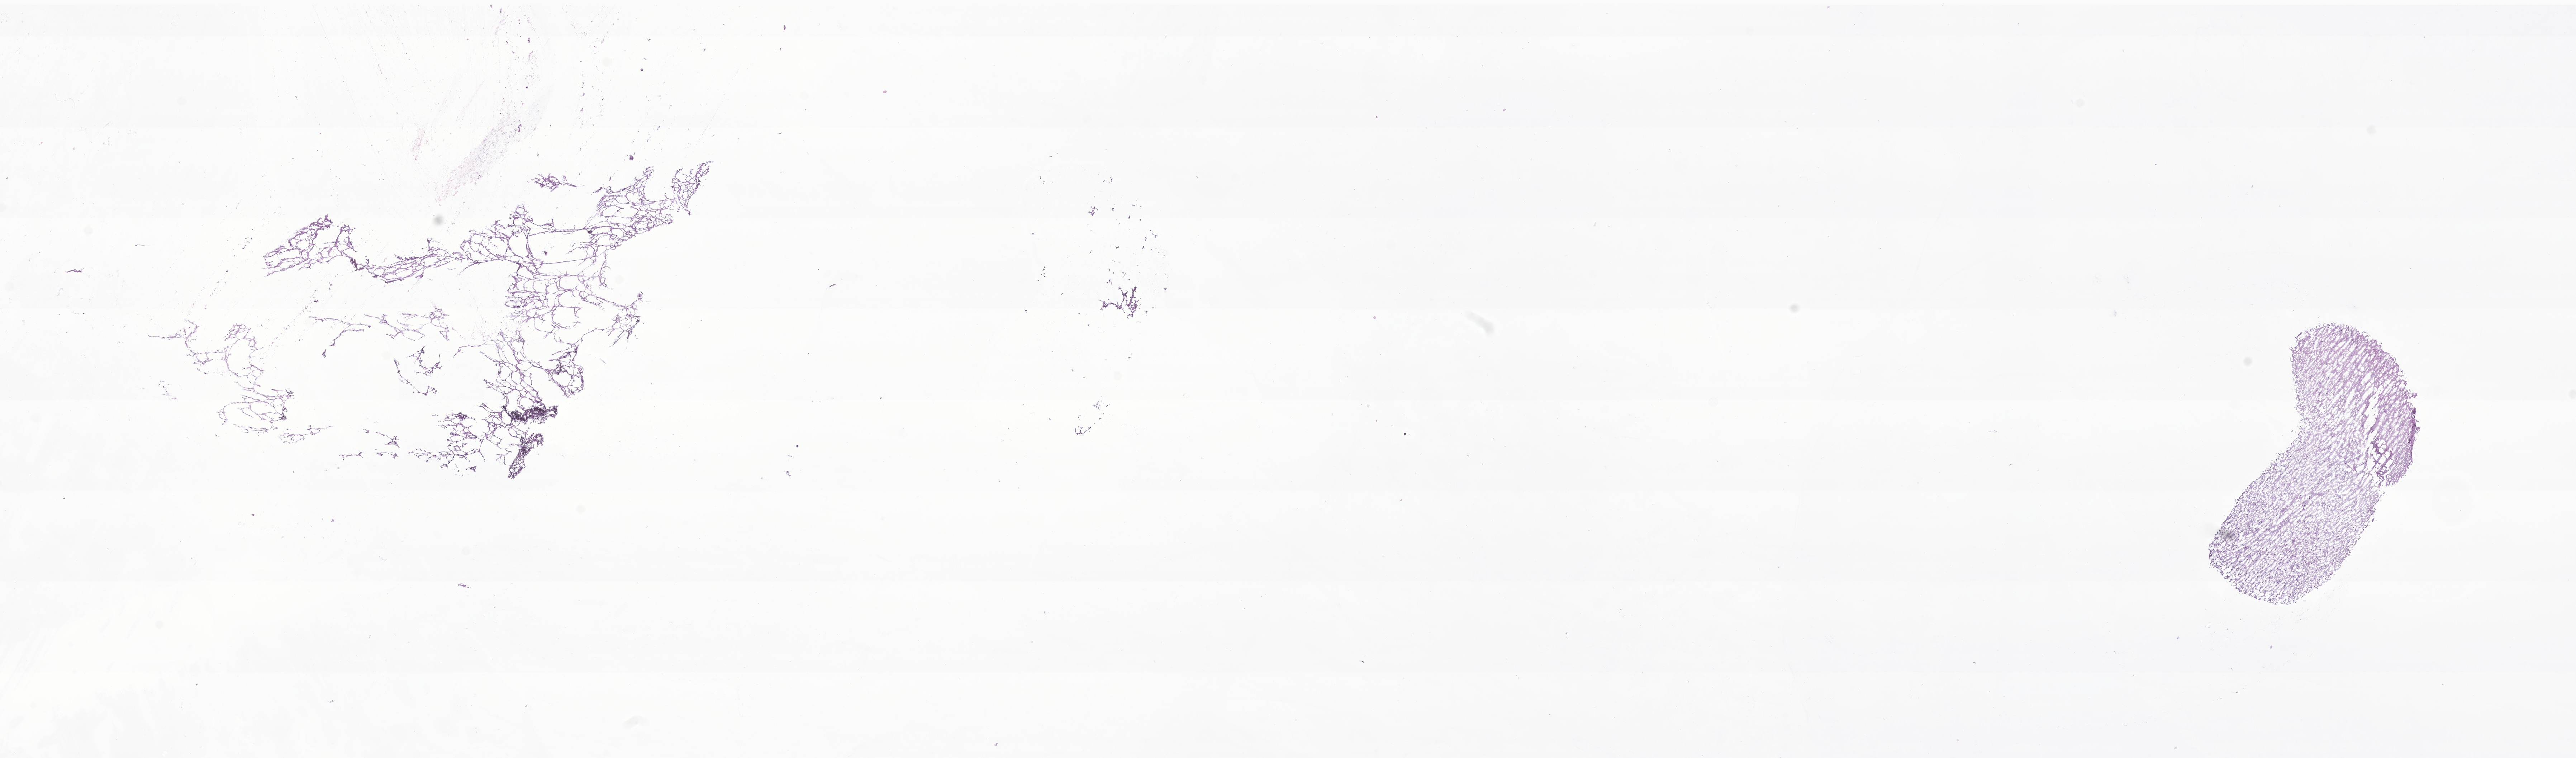
Hematoxylin and eosin (H&E) whole-slide image of tumor tissue from the temporal lobe — whole scanned area (about 30.3 x 8.9 mm) shown as a low-resolution overview; frozen section. Female patient, age 193 months (16 years 1 month).
* diagnosis (ICD-O-3 morphology term): Ganglioglioma, NOS